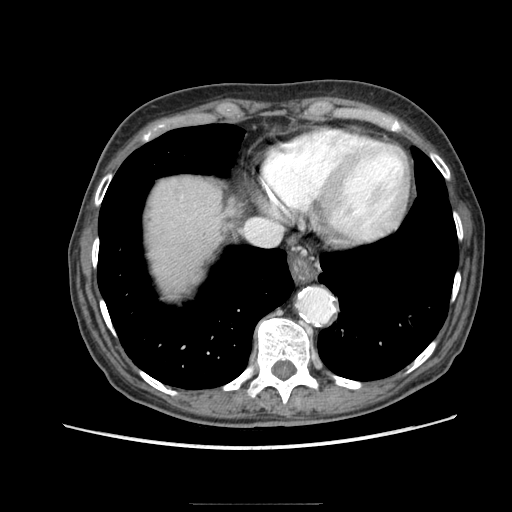
Contrast-enhanced abdominal CT (liver protocol), one axial slice; position 75 of 83 along the scan axis; reconstruction kernel STANDARD; 140 kVp; soft-tissue window (W 400 / L 40 HU); 2.5 mm slice thickness; 512 × 512 image matrix. From the clinical record (not read from this slice): diagnosis: hepatocellular carcinoma (patient treated with transarterial chemoembolisation; whether this scan precedes or follows treatment is not stated here); TNM stage (as recorded): Stage-I; Child-Pugh class: A; tumour differentiation: moderately differentiated; tumour nodularity: uninodular.
Structures marked on this image (semi-automatic segmentation, software-assisted and operator-edited):
- liver parenchyma outside the tumour (the mass and vessels are separate outlines, so this box may not span the whole liver): bounding box <148,178,222,294> (left, top, right, bottom; pixels)